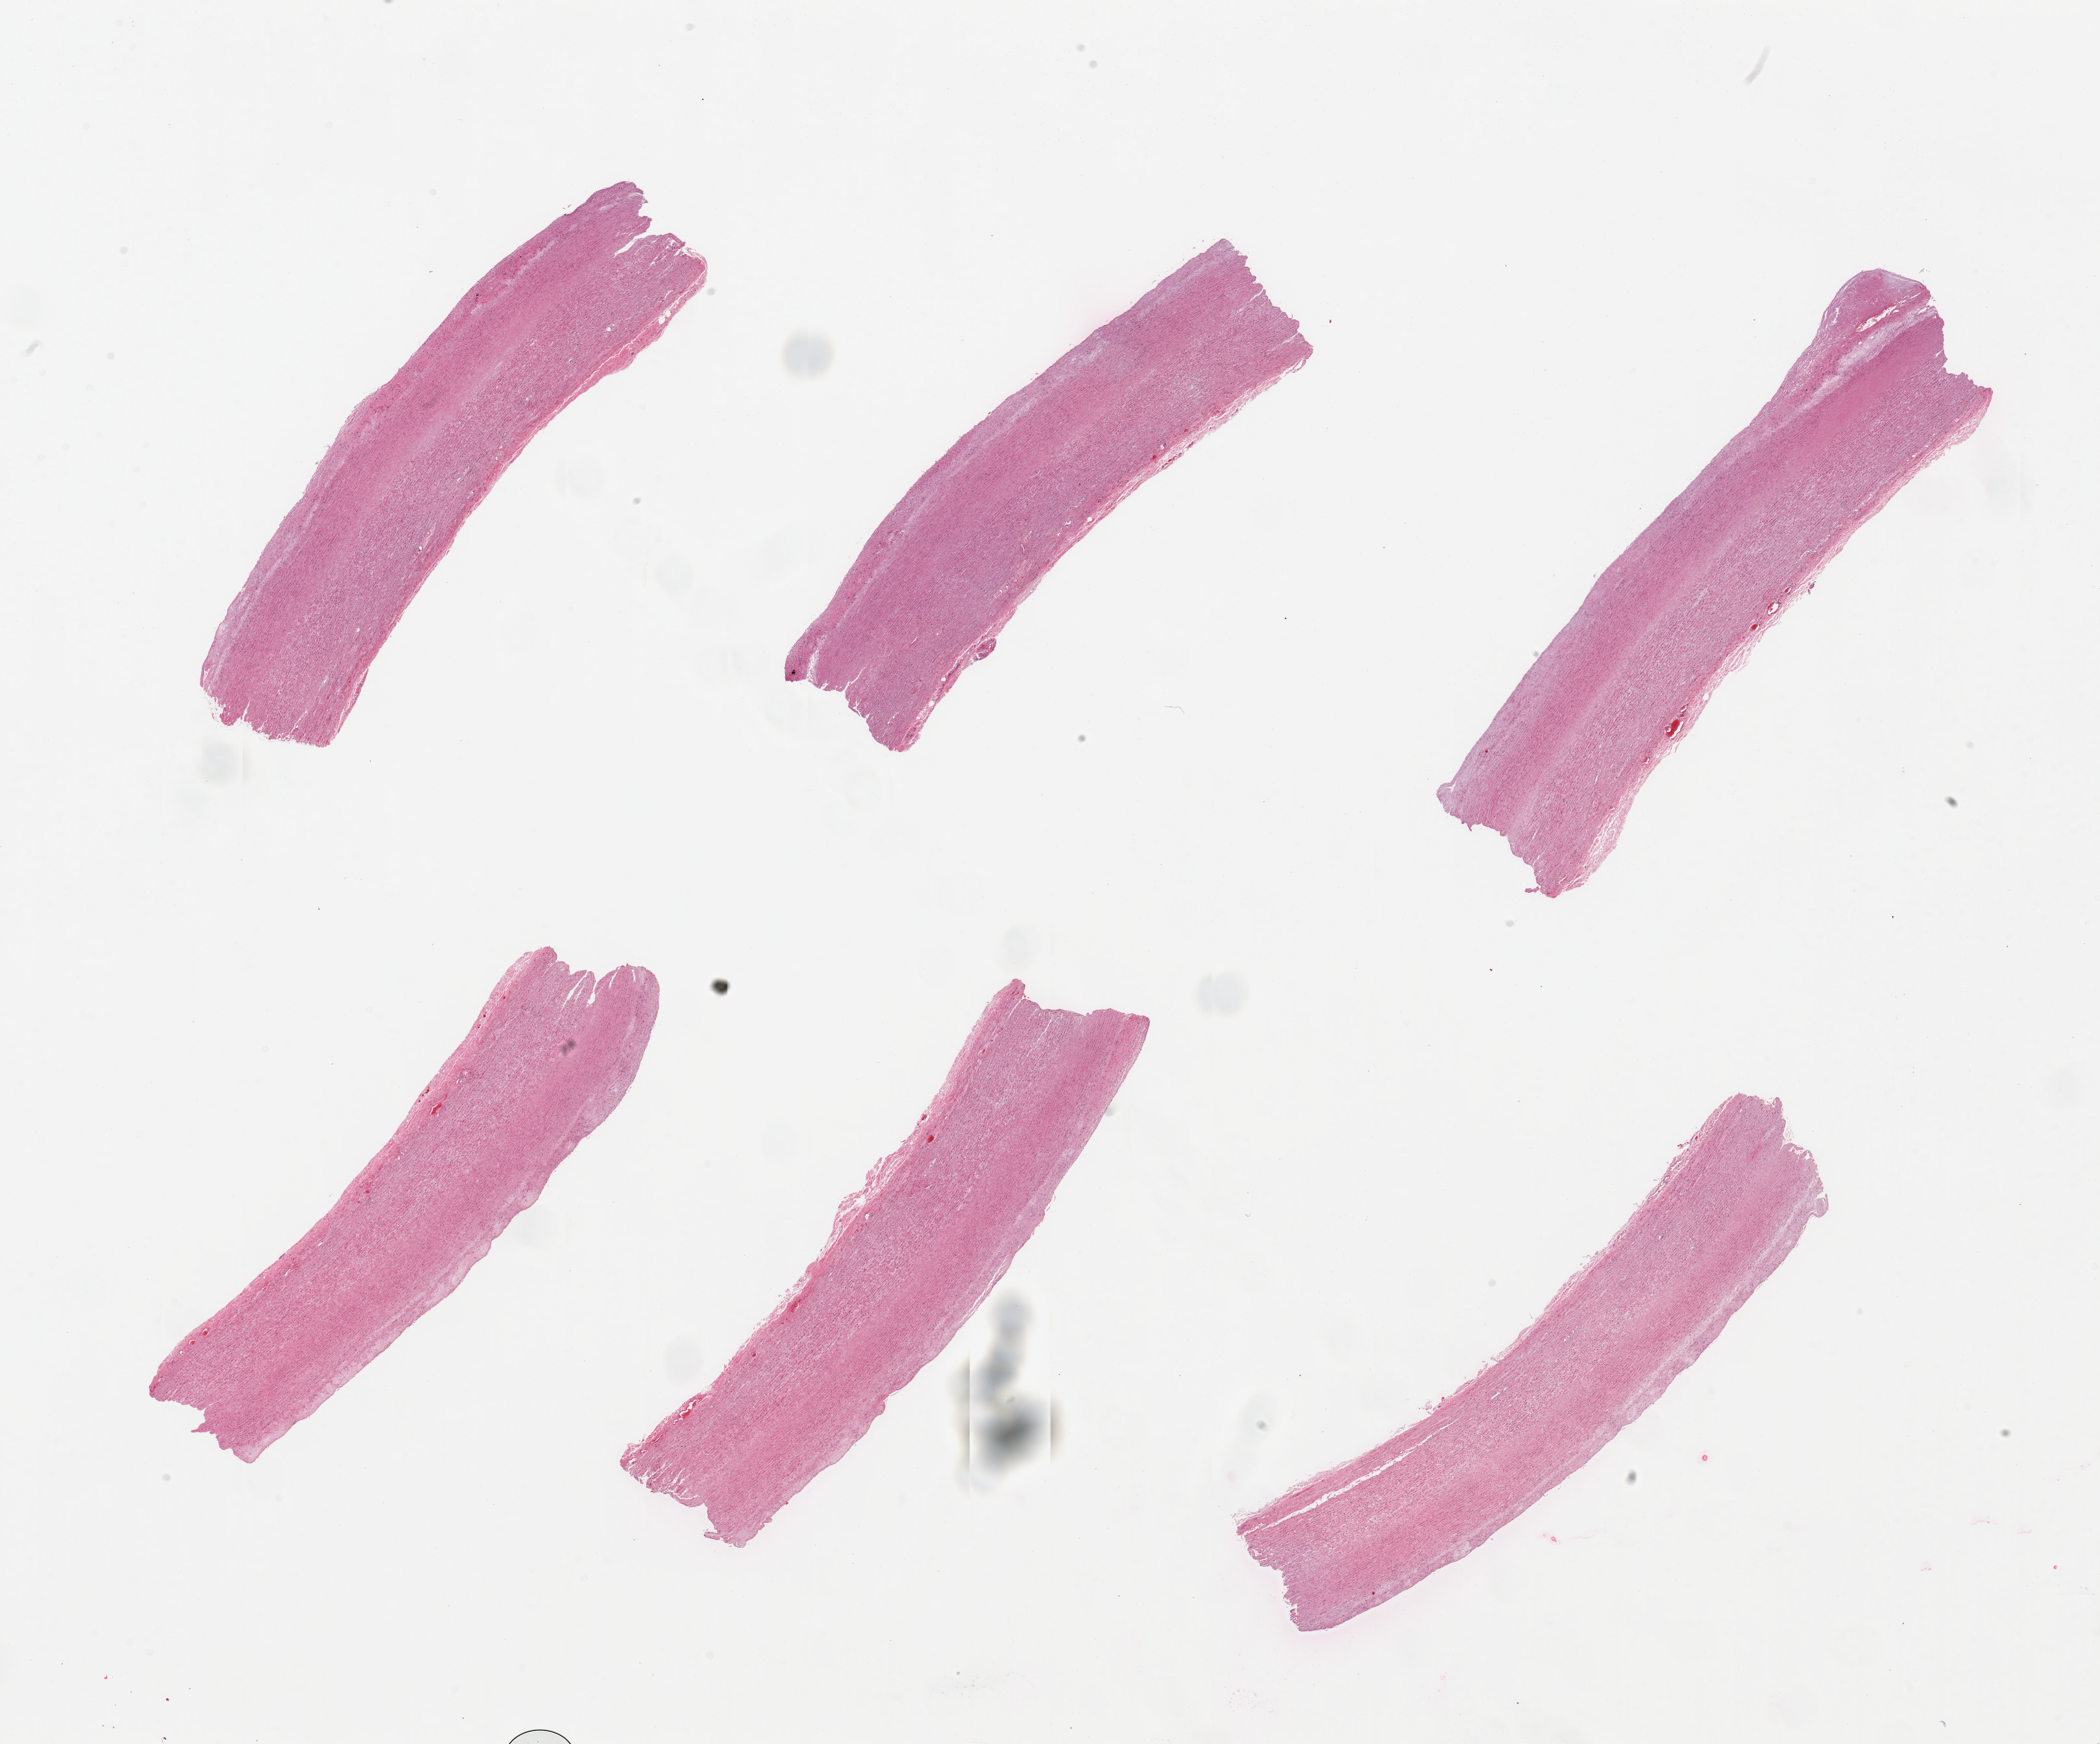
Whole-slide image, hematoxylin and eosin (H&E) stain, a low-resolution overview of the entire scanned area, about 25.6 x 21.3 mm (slide scanned at 20x). PAXgene-fixed, paraffin-embedded tissue. Target tissue: aorta. Donor tissue sample. Donor sex: male.
Reviewer comment on this tissue sample: 6 pieces, atherosis up to ~0.3mm.